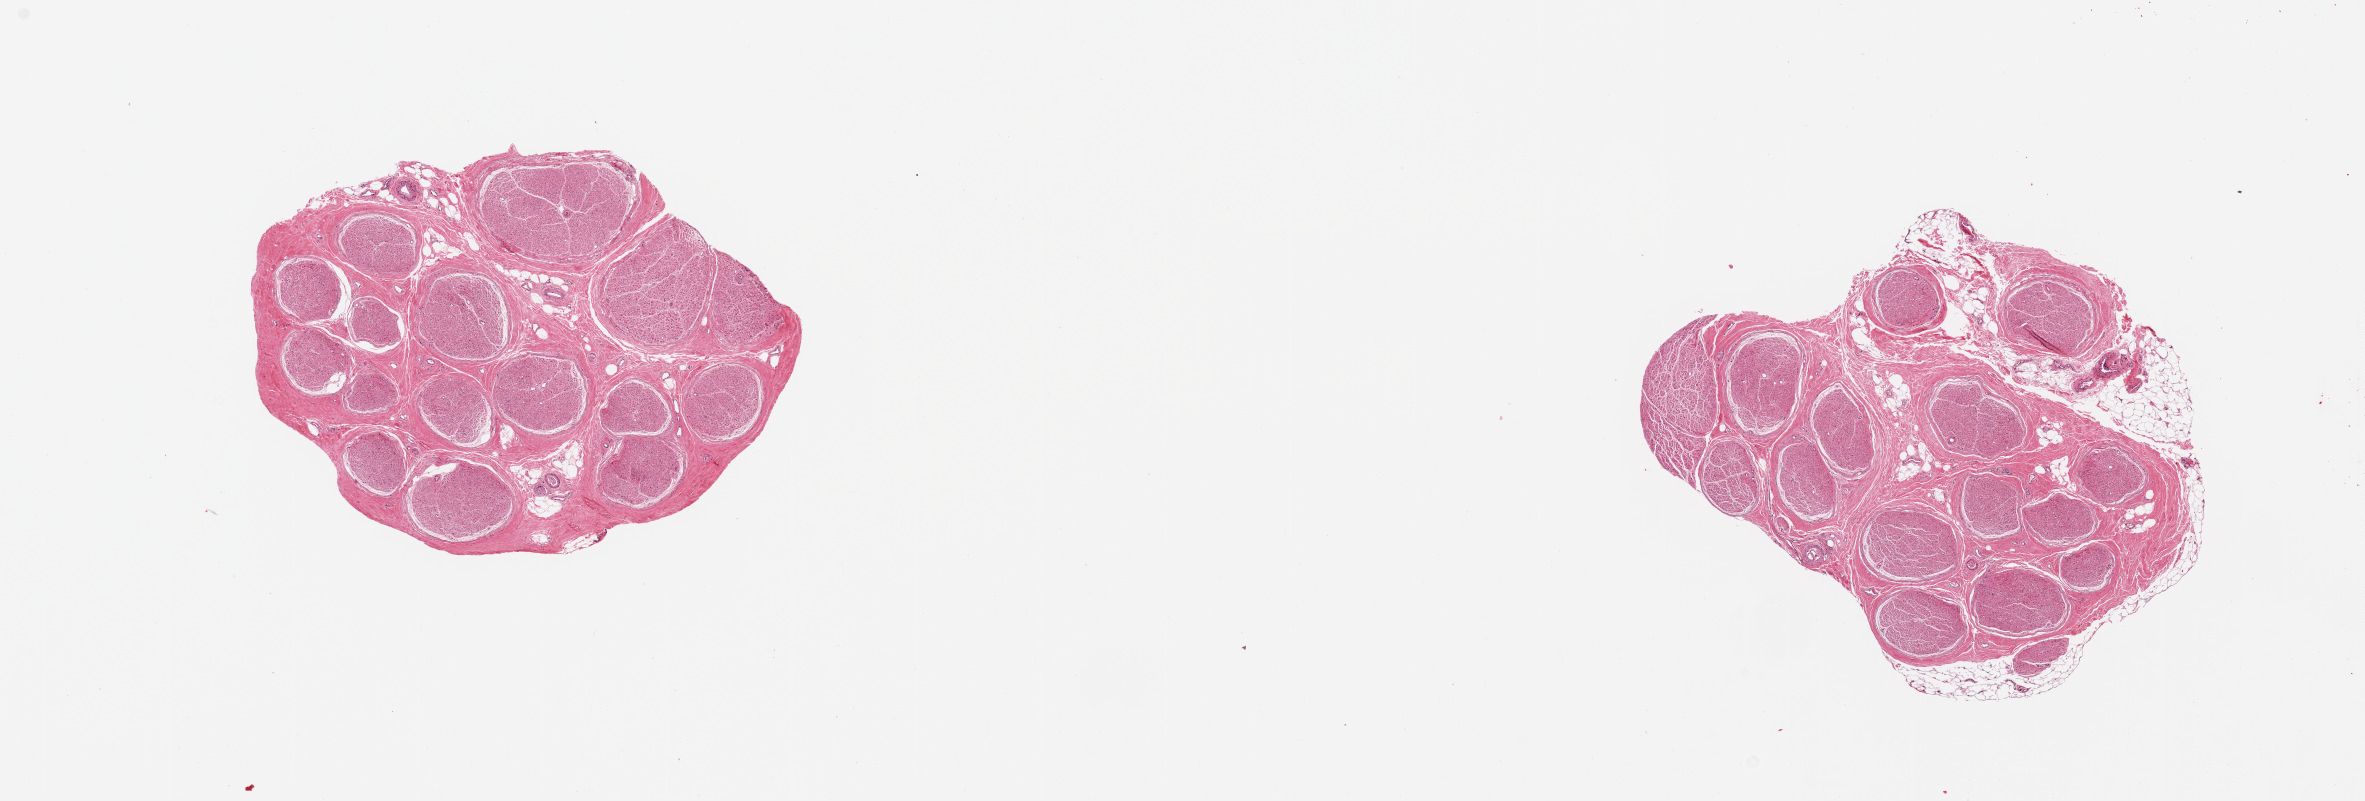
Digitized H&E-stained section, brightfield — a low-resolution overview of the entire scanned area, about 18.7 x 6.3 mm. PAXgene-fixed paraffin-embedded (PFPE) section. Sampled site (target tissue): tibial nerve. Donor tissue sample. Donor: male.
Review note (as recorded): 2 pieces; 10% peripheral fat in 1 piece.